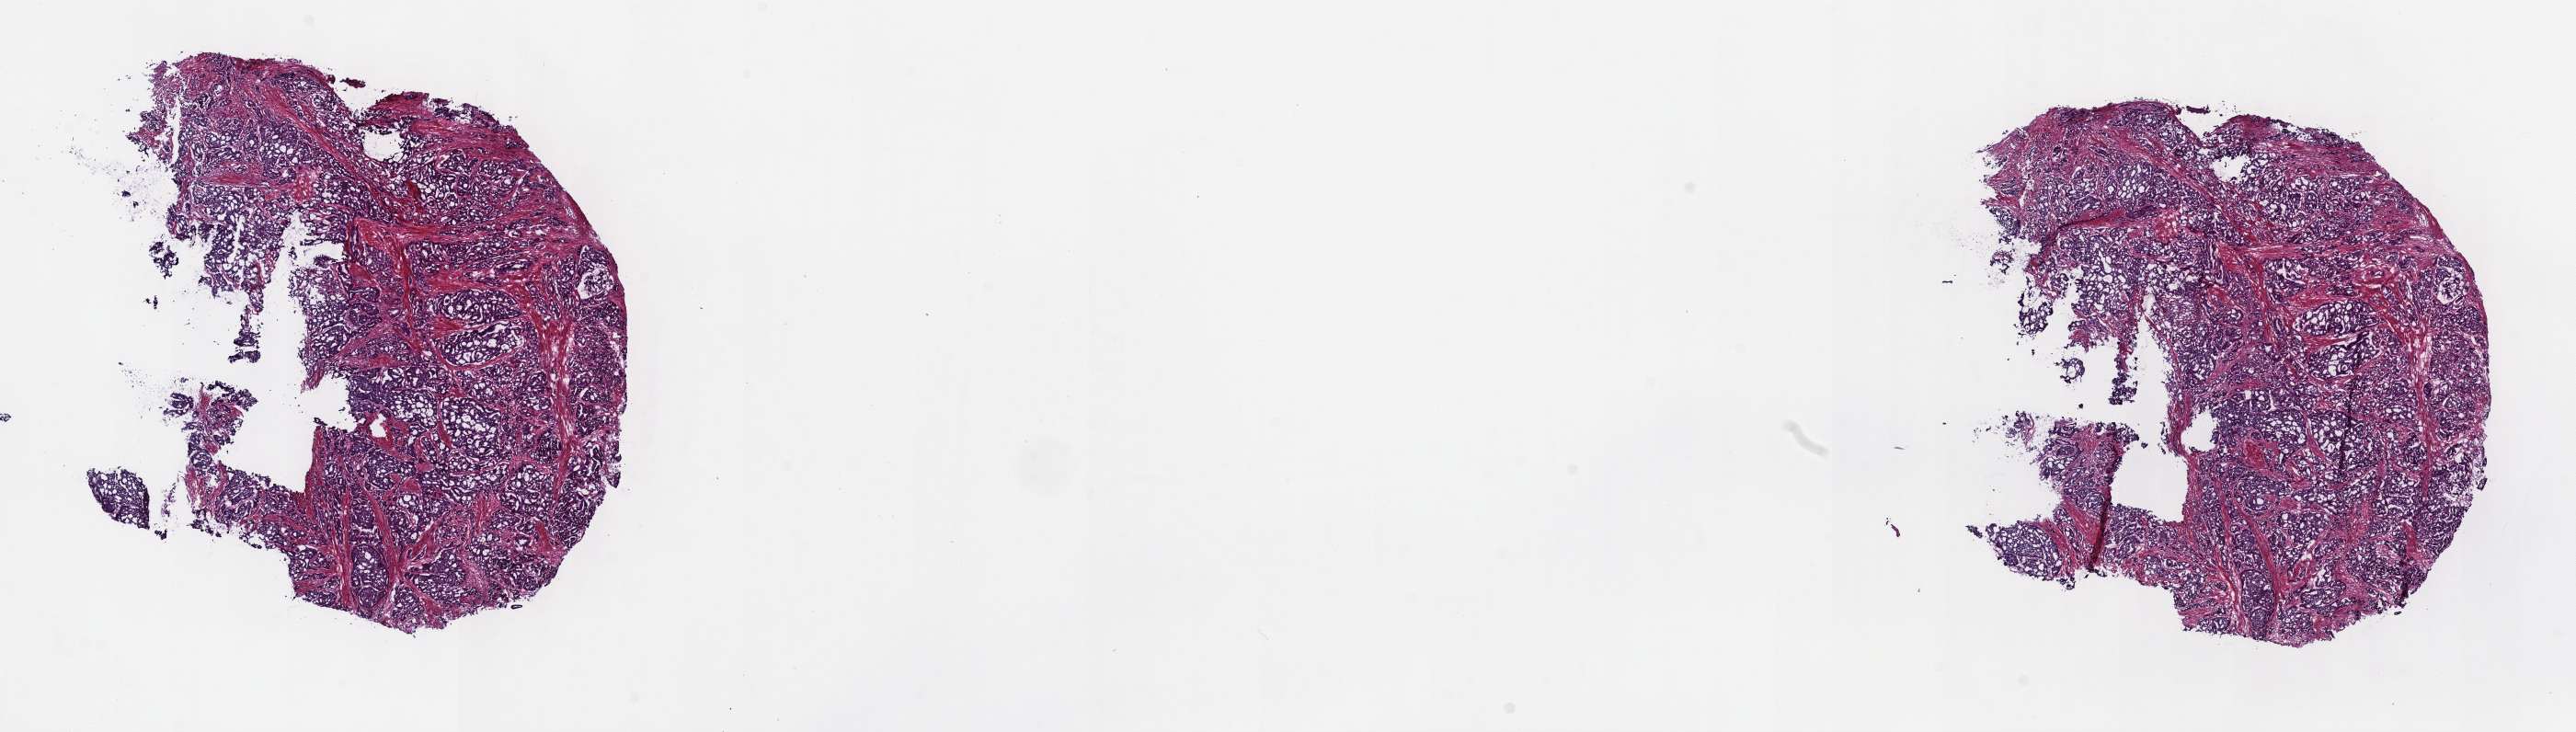
Hematoxylin and eosin (H&E) stained whole-slide image, low-resolution overview of the scanned area, about 22.7 x 6.4 mm; frozen section from the top of the tissue portion; sample: primary tumour, prostate. Male, age 70 years at initial diagnosis. Gleason score: 8 (4+4). Pathologist review of this section (percent, as recorded): tumour cells 57%, tumour nuclei 92%, normal cells 0%, stromal cells 40%, necrosis 3%. Infiltration values recorded for this section: lymphocyte infiltration 4%, monocyte infiltration 1%, neutrophil infiltration 1%.
- pathologic diagnosis: Adenocarcinoma, NOS (prostate gland)
- laterality: bilateral
- lymph nodes positive (case pathology): 0 of 16 examined